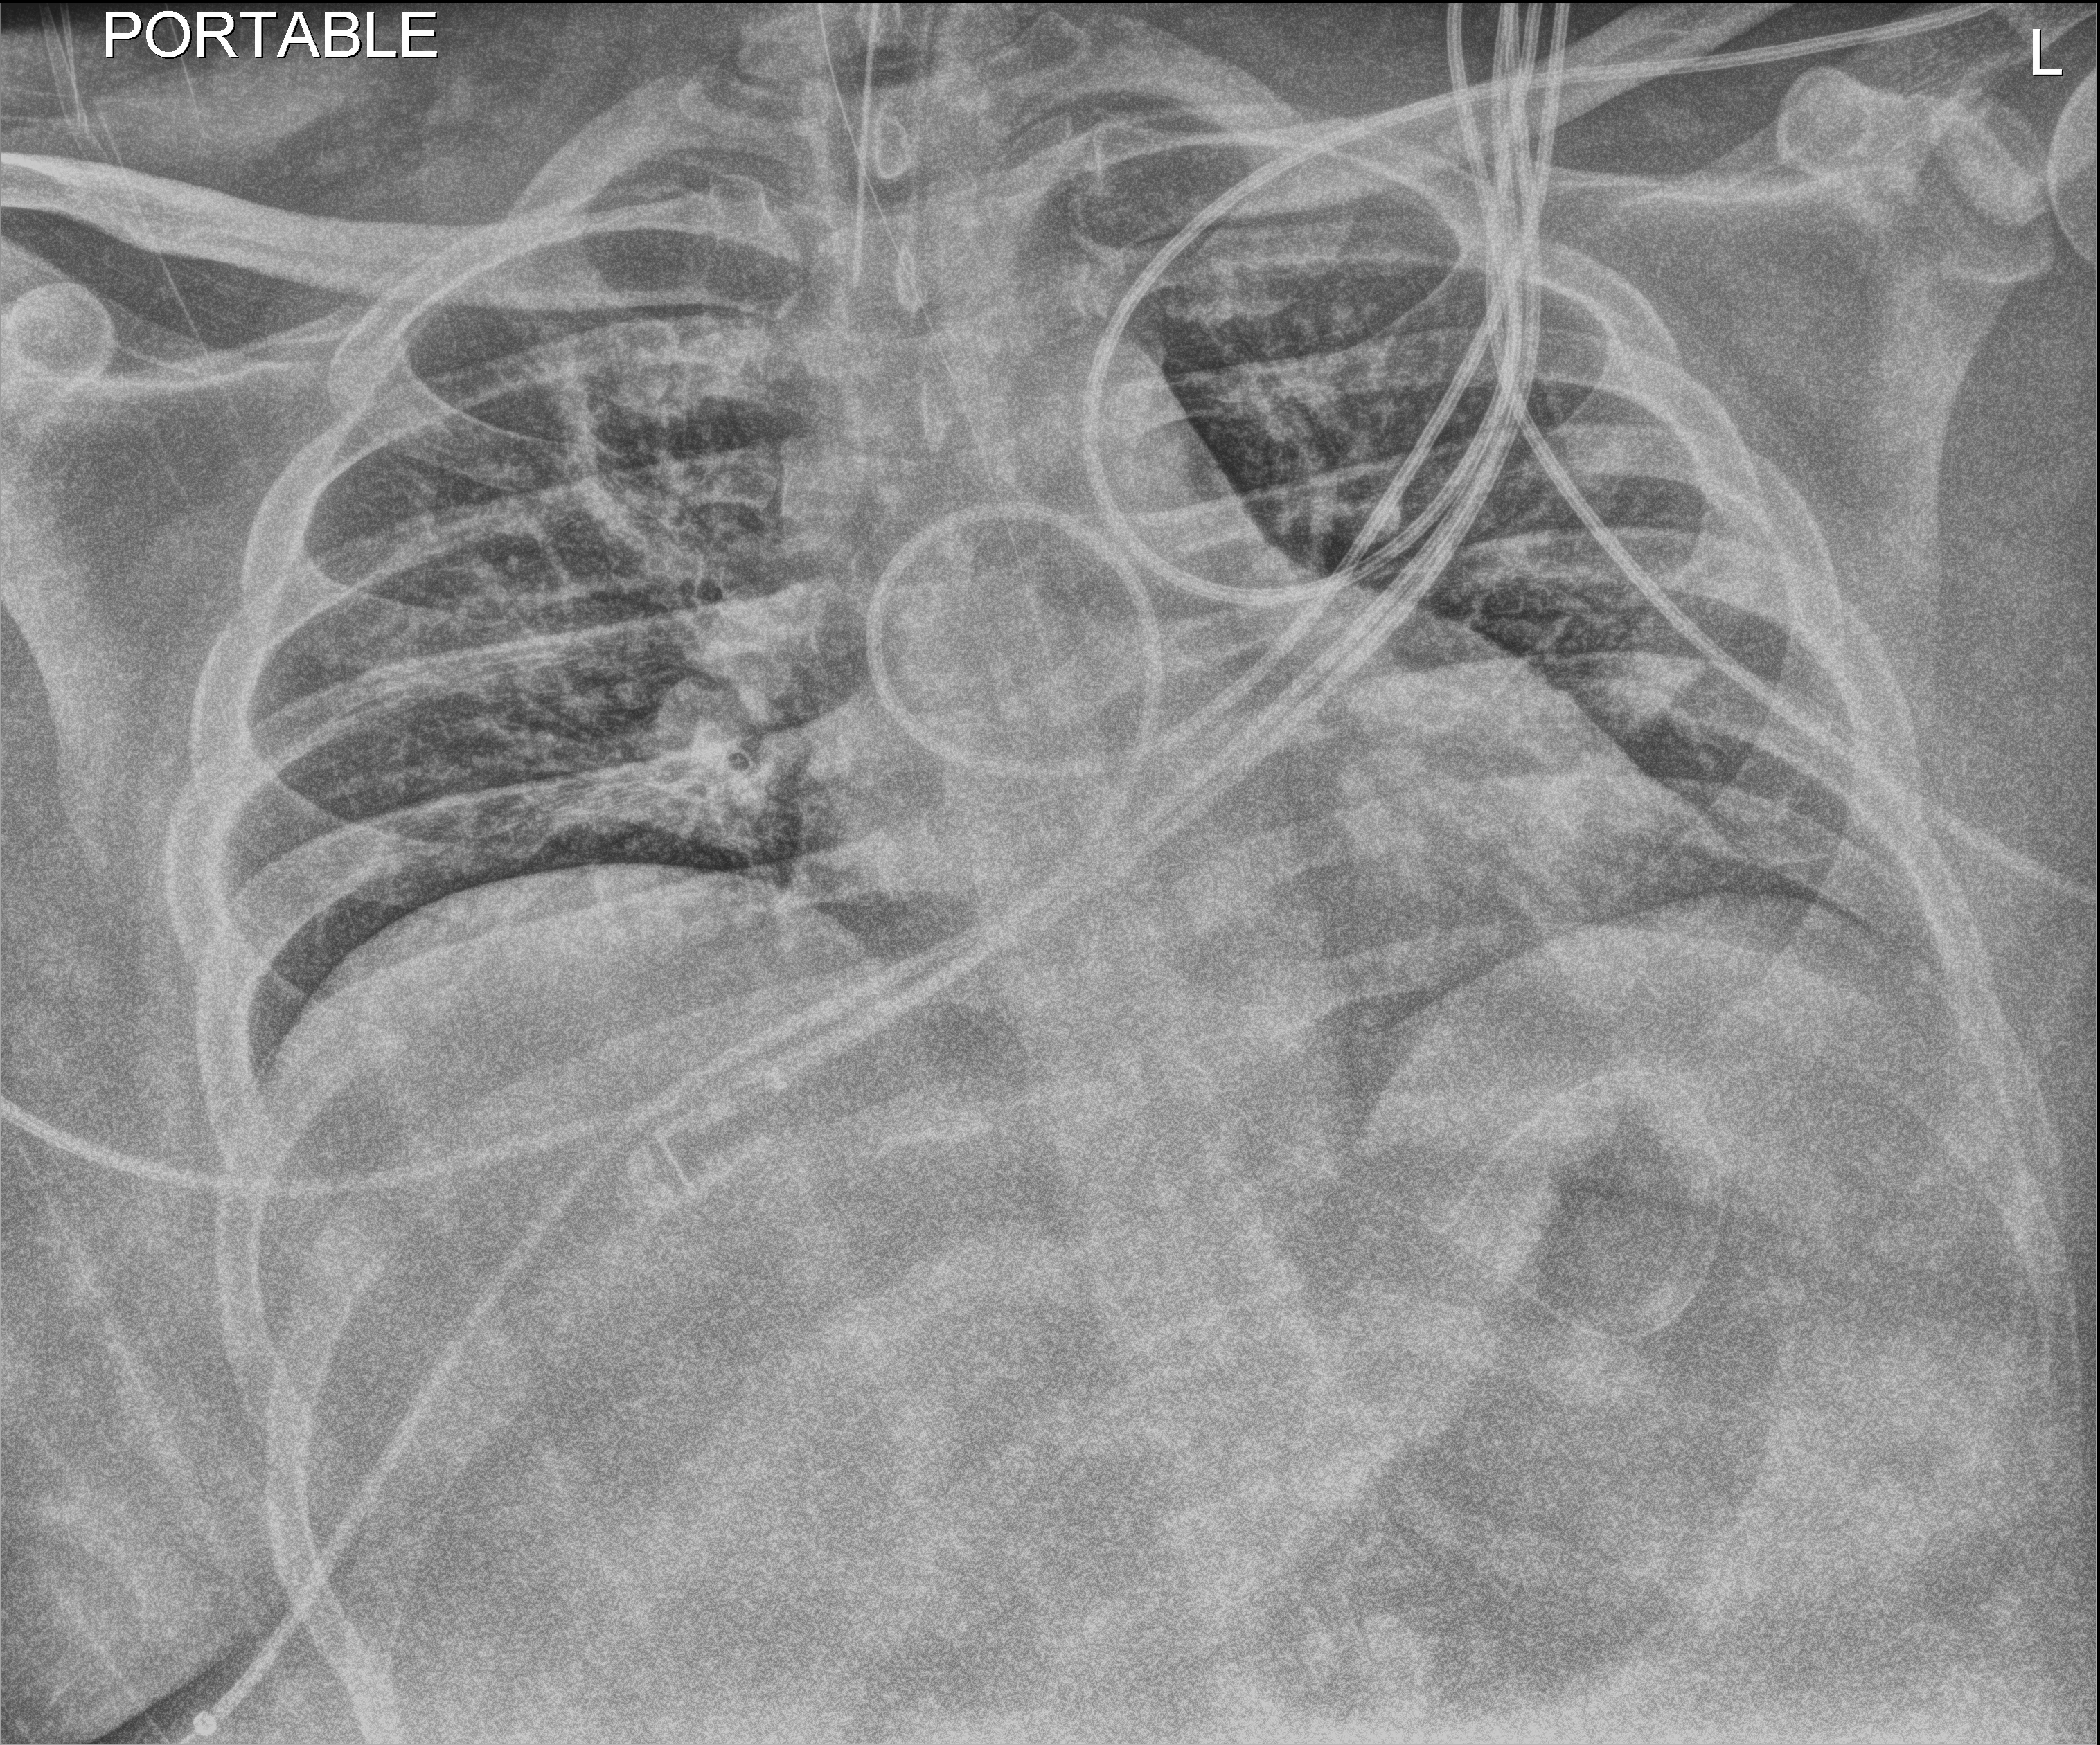
Chest X-ray (portable), anteroposterior (AP) projection. Male patient hospitalised with COVID-19, age 18–59 years.
Hospital-stay facts (about this admission, not read from this image; timing relative to this image not recorded):
- other chronic lung disease (admission record): yes
- mechanically ventilated during this hospital stay: yes
- smoking status (admission record): never